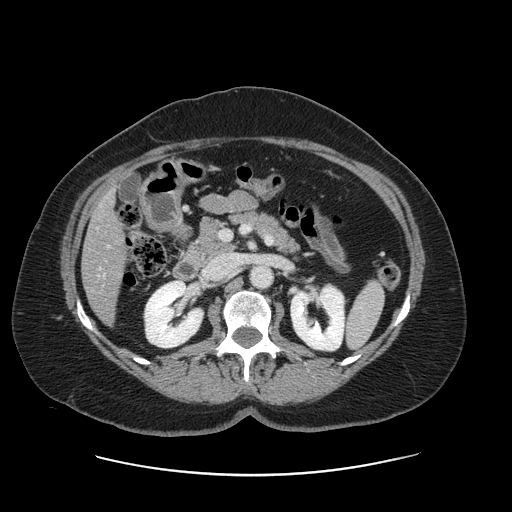
Contrast-enhanced abdominal CT, one axial slice; position 61 of 161 along the scan axis; intravenous contrast given; soft-tissue window (W 400 / L 40 HU); 2.5 mm slice thickness; 512 × 512 image matrix, field of view 398 × 398 mm. Female patient, age 62 years. Case-level facts recorded for this patient, not image findings: diagnosis: colorectal cancer liver metastases, imaged before liver resection; multiple liver metastases: no; largest metastasis: 2.5 cm; disease in both lobes: no.
Structures marked on this image (outlined manually by an expert reader):
- liver: bounding box [x1, y1, x2, y2] px = [83, 193, 125, 322]